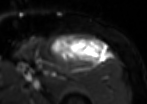
MRI of an extremity soft-tissue mass, one axial slice. Position 71 of 85 along the scan axis. T2-weighted fat-saturated. MR volume resampled by the dataset authors to the PET/CT grid (not the native acquisition matrix). 3.27 mm slice thickness. 147 × 104 image matrix, field of view 144 × 102 mm. Male patient. From the clinical record (not read from this slice): histological type: extraskeletal osteosarcoma; grade: high; site of the primary tumour: thigh.
Outlined on this slice (expert contour drawn on MRI and transferred to this co-registered scan by the dataset authors):
- gross tumour volume (mass): bounding box (x1, y1, x2, y2) in pixels: (51, 35, 107, 66)